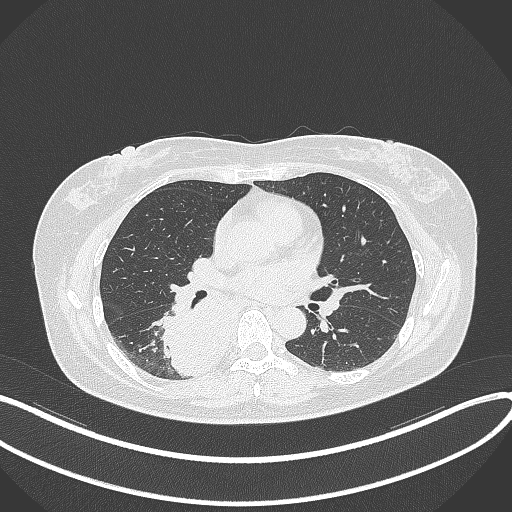
Chest CT, one axial slice. Position 189 of 331 along the scan axis. 120 kVp. Lung window (W 1500 / L -600 HU). 1 mm slice thickness. 512 × 512 image matrix, field of view 400 × 400 mm. Patient: female, 54 years. From the clinical record (not read from this slice): clinical TNM (as recorded): T4 N0 M0.
Annotated regions visible in this slice (rectangle marked by the reading radiologist):
- lung tumour (recorded histology: adenocarcinoma): bounding box (x1, y1, x2, y2) in pixels: (152, 278, 235, 381)